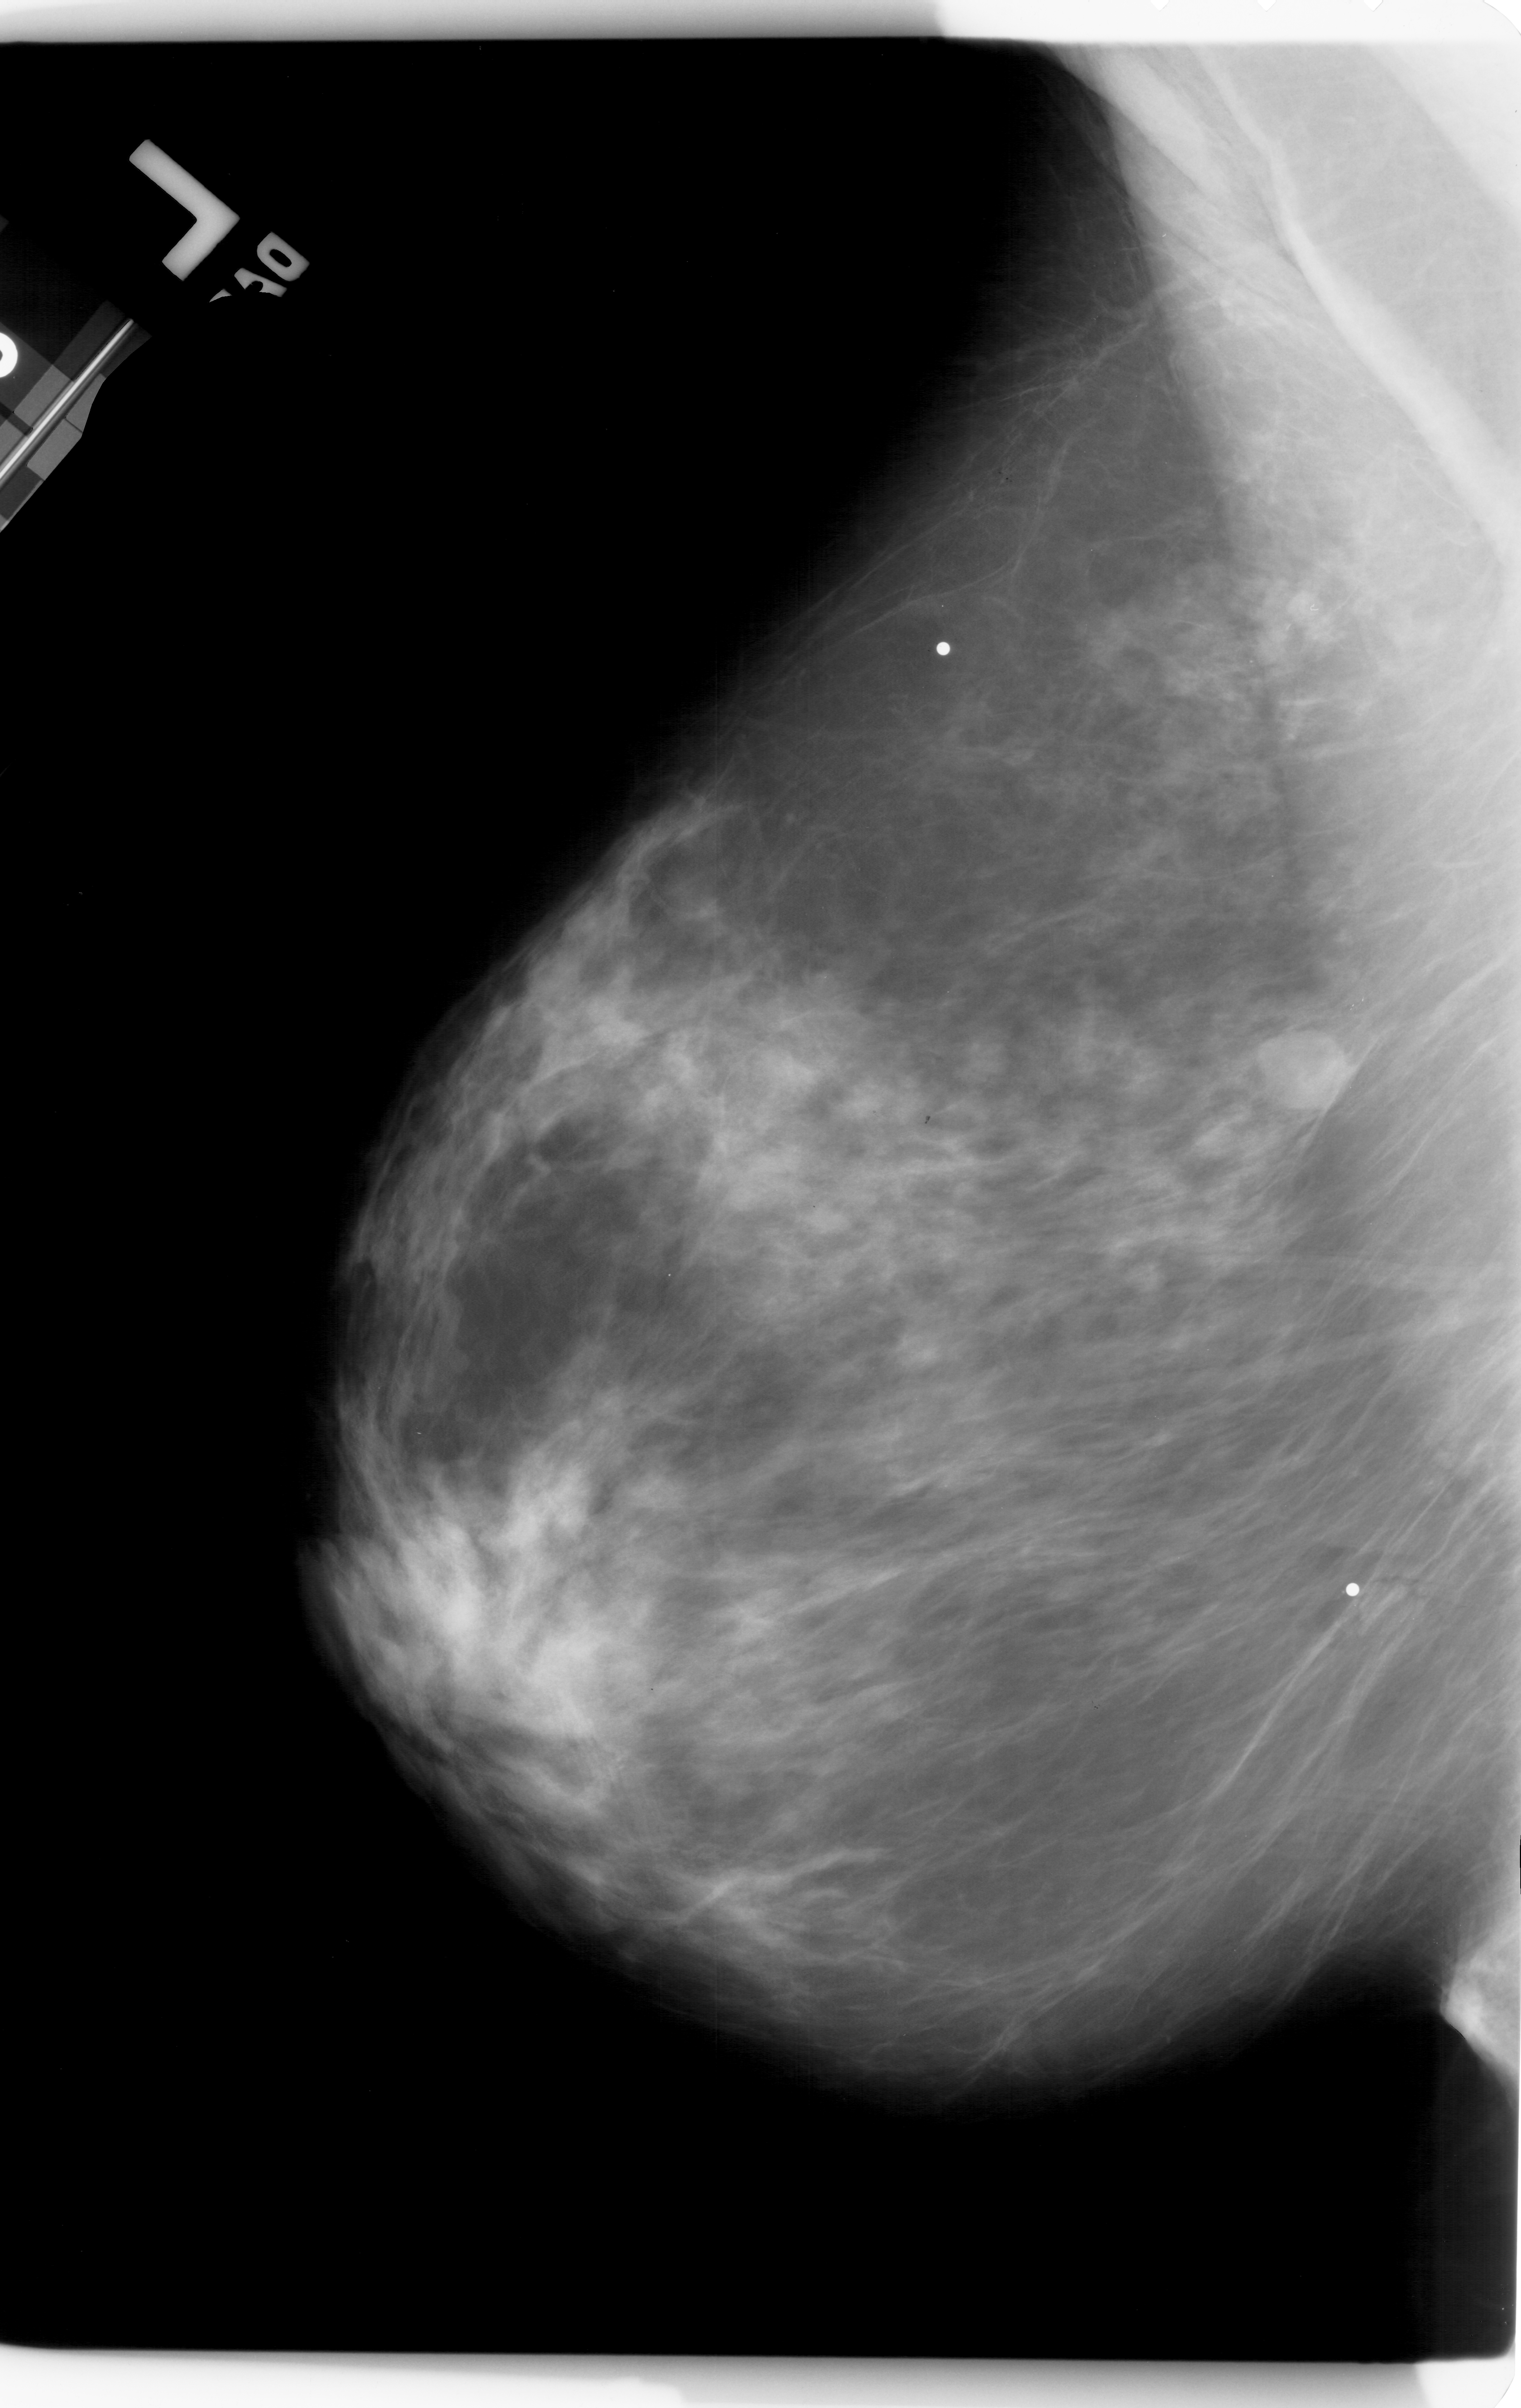
Digitized screen-film mammogram, left breast, MLO view, breast composition: heterogeneously dense (BI-RADS density category 3 of 4).
Finding: mass, shape lobulated, margins obscured; BI-RADS assessment category 4; subtlety rating 3 on a 1 (subtle) to 5 (obvious) scale; pathology (as recorded): malignant.